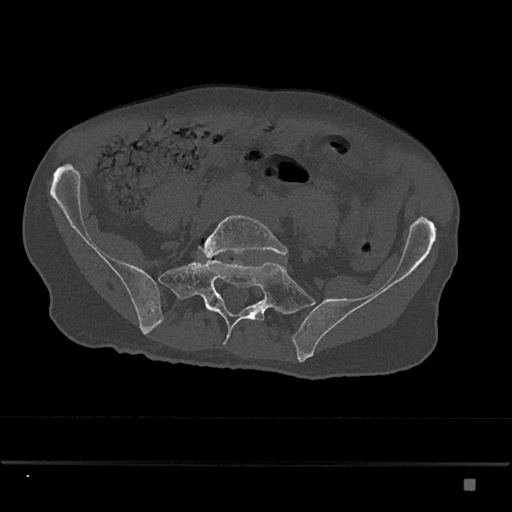
CT including the spine, one axial slice. Slice 238 of 797 in the series (ordered by position). 120 kVp. Bone window (W 1800 / L 400 HU). 512 × 512 image matrix, field of view 390 × 390 mm. Patient: male, 72 years. Case-level facts recorded for this patient, not image findings: primary cancer: prostate.
Outlined on this slice (semi-automatically segmented with operator editing):
- L5 vertebra: bounding box [x1, y1, x2, y2] px = [199, 215, 288, 258]